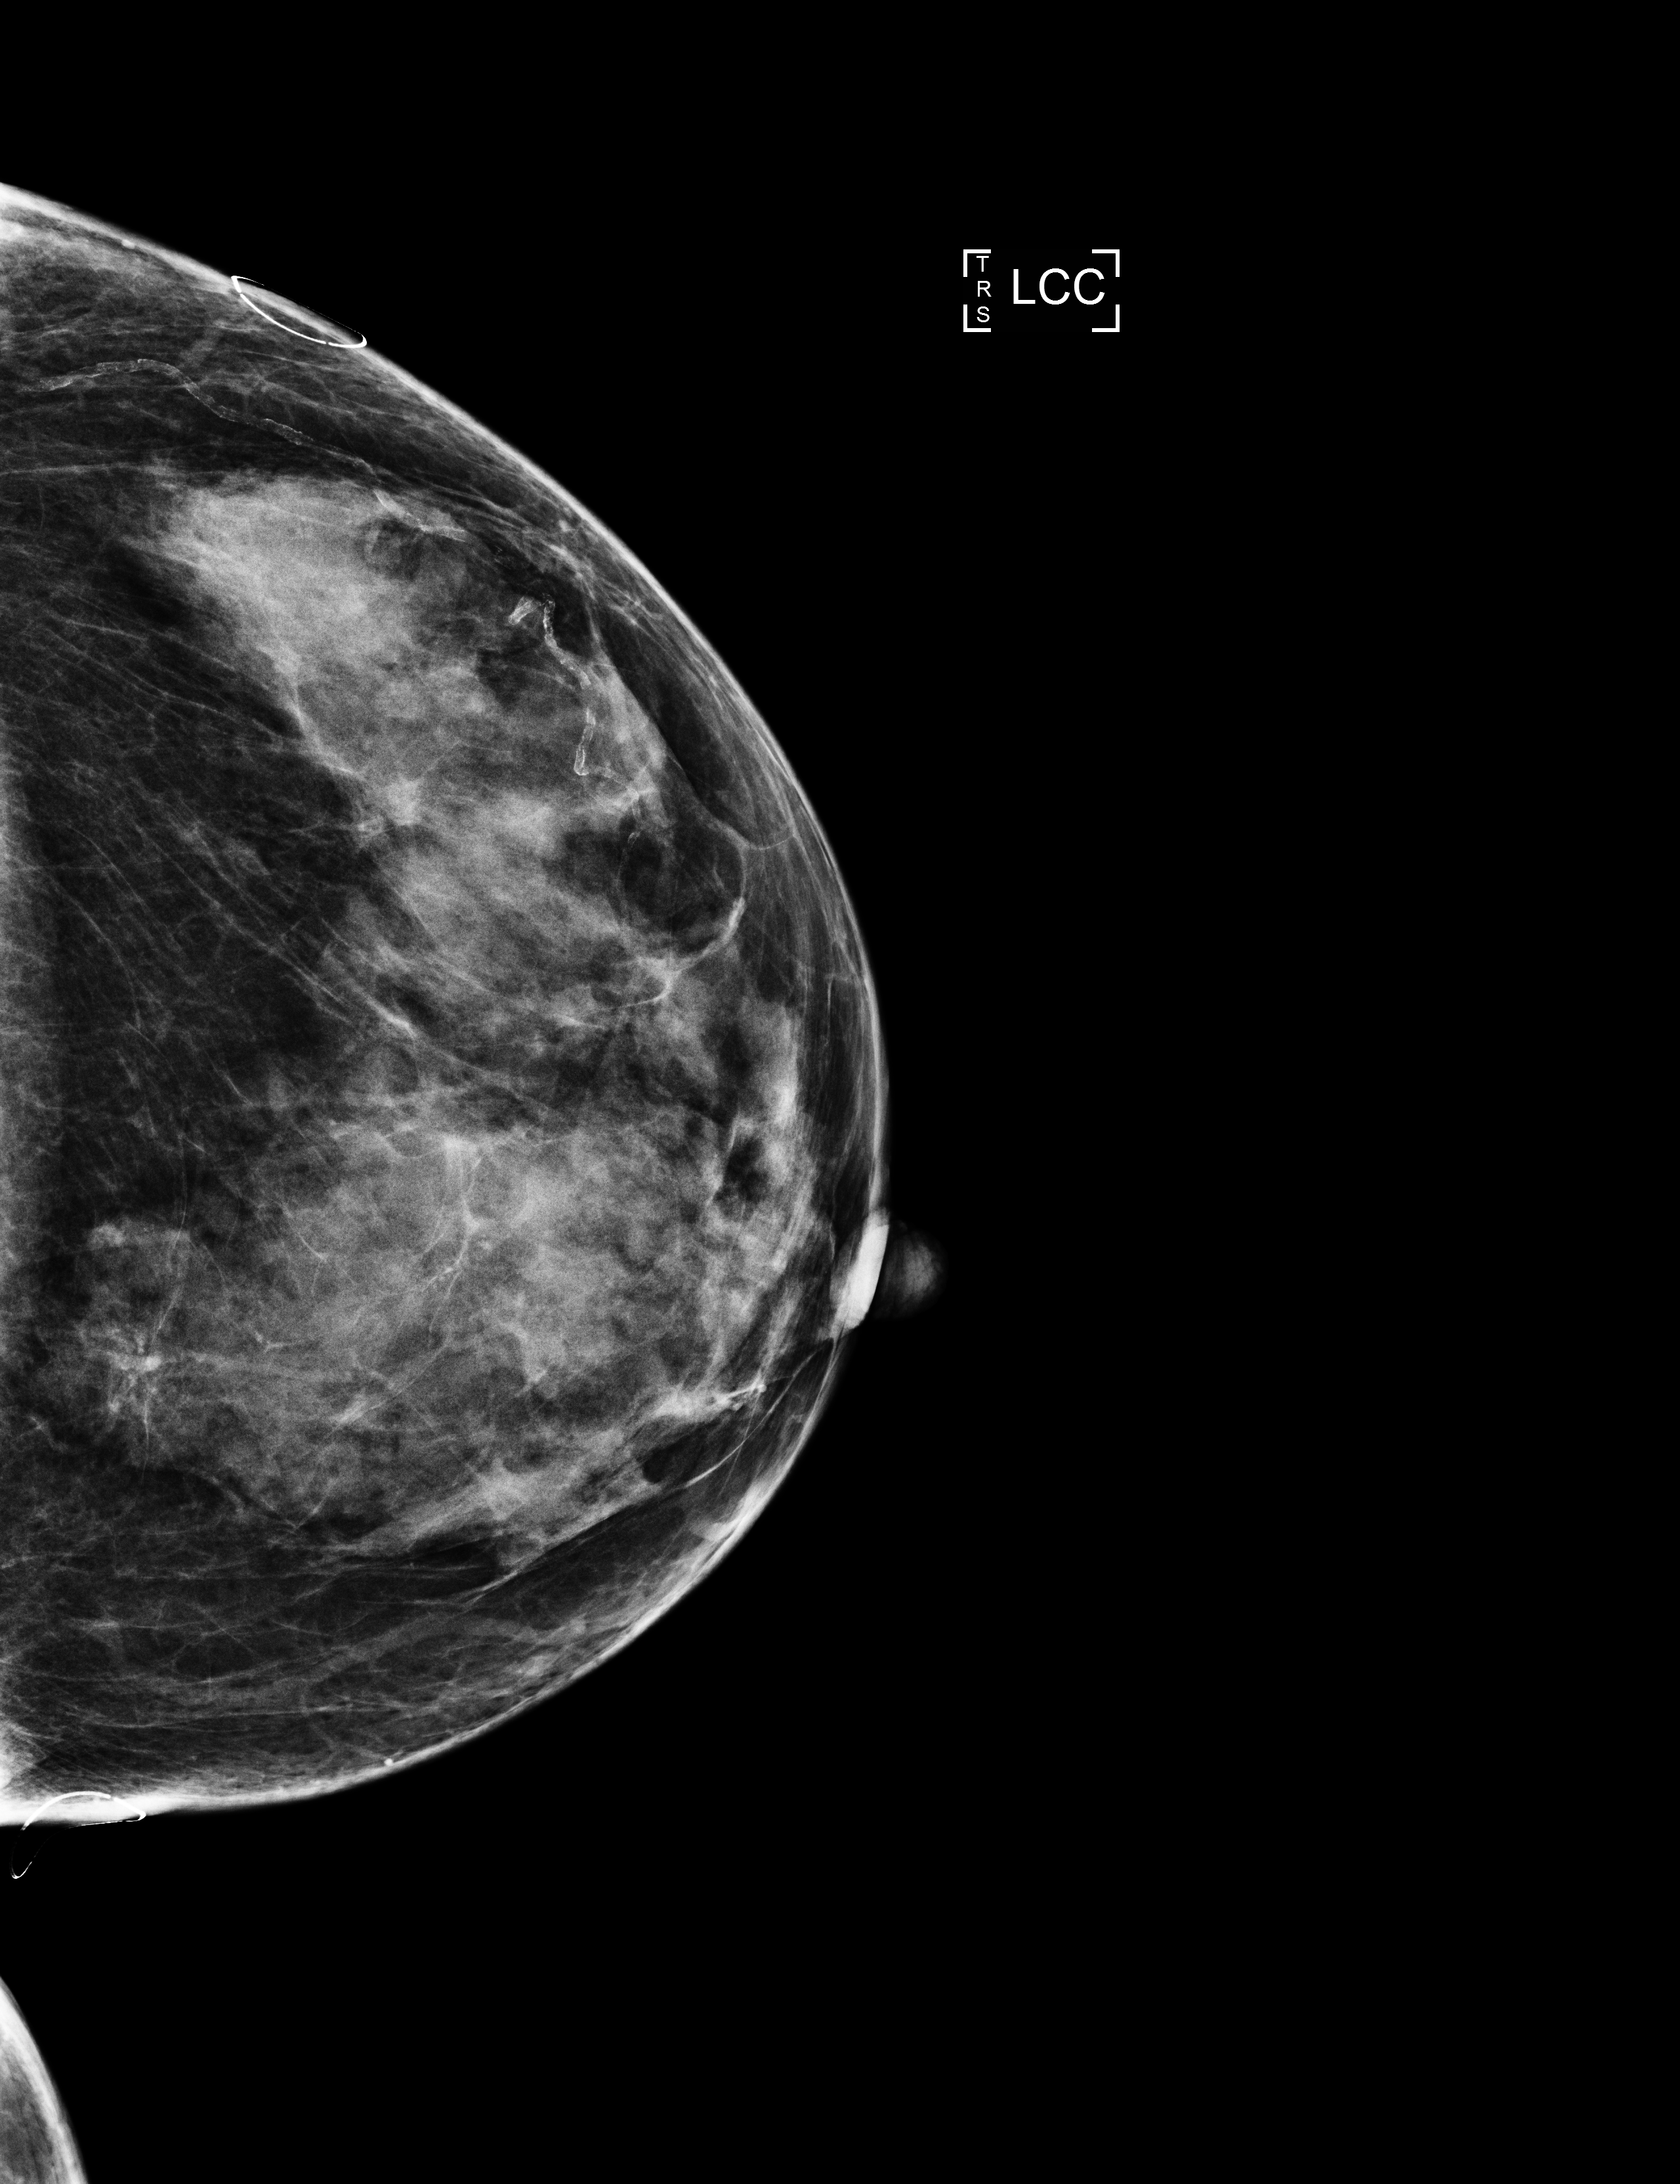
Annual screening mammography examination; compressed breast thickness 41 mm. Patient: female, 75 years.
Image type: full-field digital mammogram. Breast: left. Projection: cranio-caudal projection.